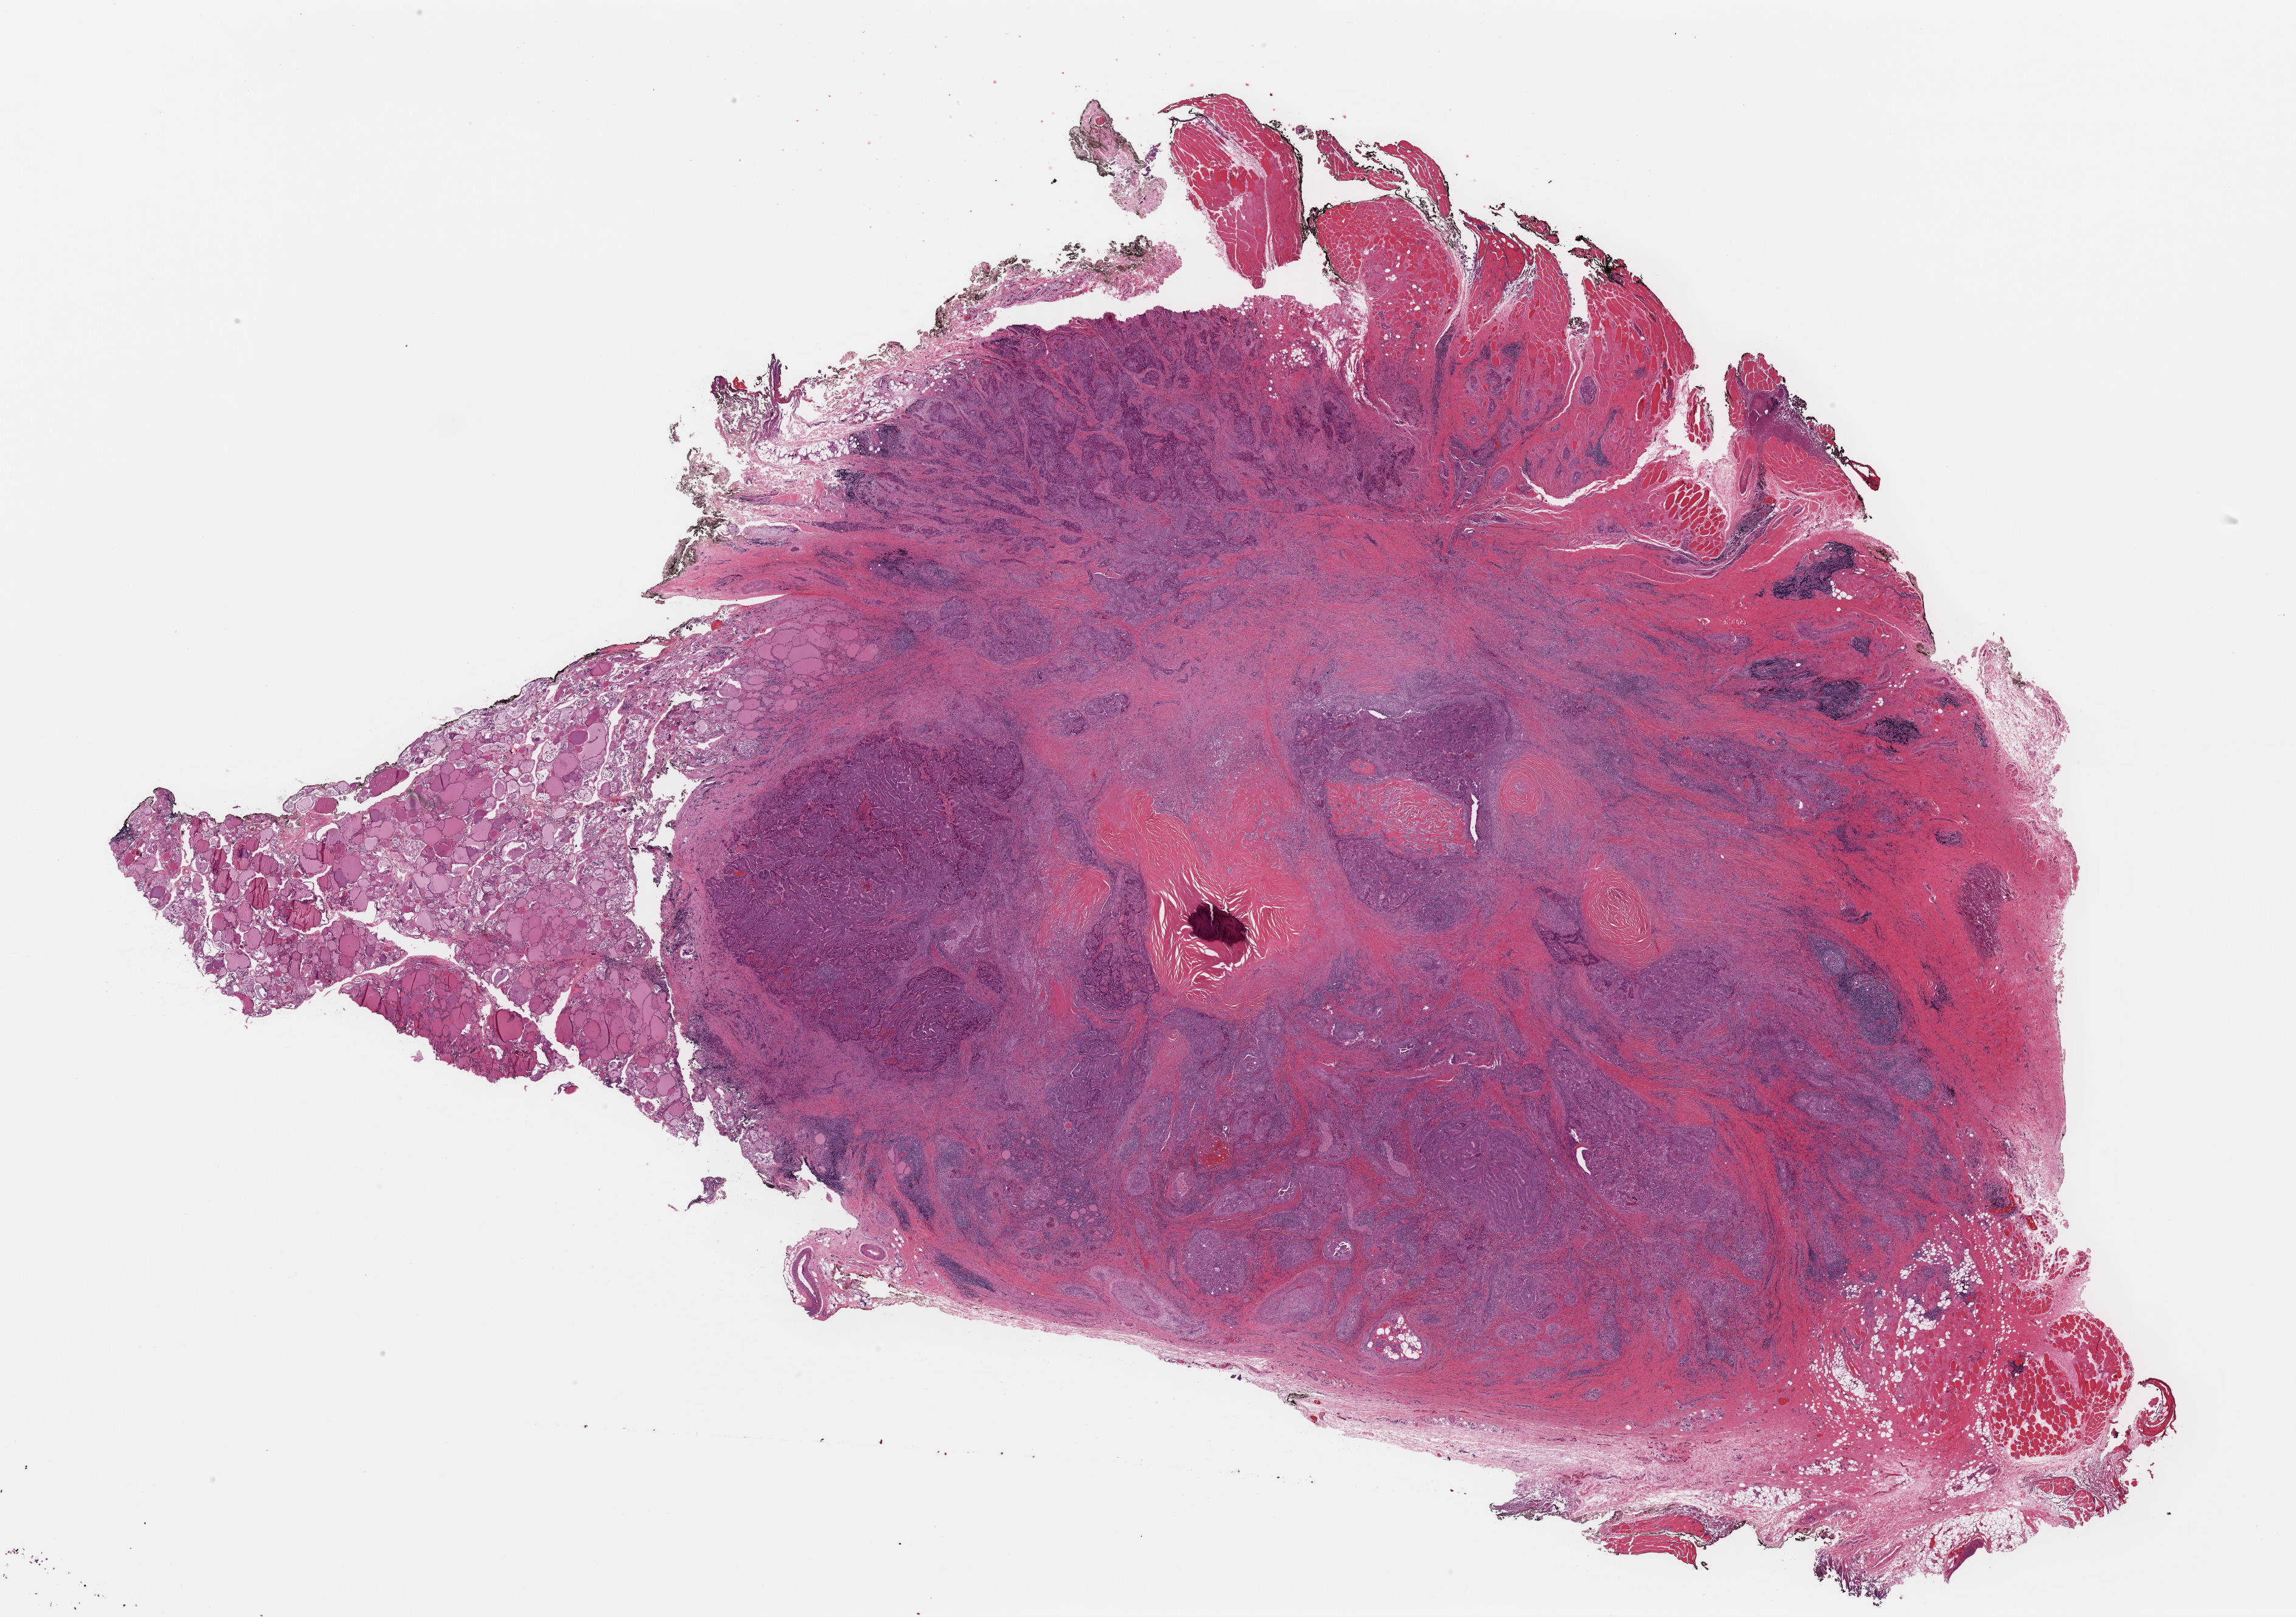
Whole-slide histology image, H&E-stained, a low-resolution overview of the entire scanned area, about 29.8 x 21.0 mm (slide scanned at 40x), formalin-fixed paraffin-embedded (FFPE) diagnostic section, sample: primary tumour, thyroid. Patient: male, age at initial diagnosis 51 years.
Lymph nodes positive (case pathology): 6 of 42 examined. Laterality: right. Pathologic diagnosis: Papillary adenocarcinoma, NOS (thyroid gland). AJCC pathologic stage: IVA (7th edition).